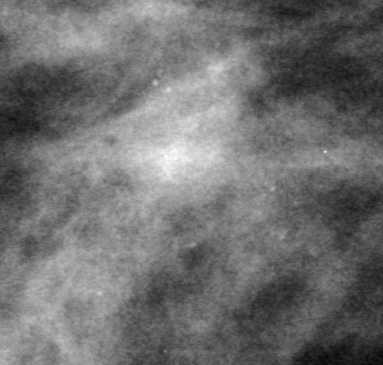
Region of interest cut from a scanned film mammogram (one marked finding), right breast, MLO view.
- Finding: mass, shape round, margins obscured; BI-RADS assessment category 0 (incomplete: needs additional imaging); pathology (as recorded): benign.